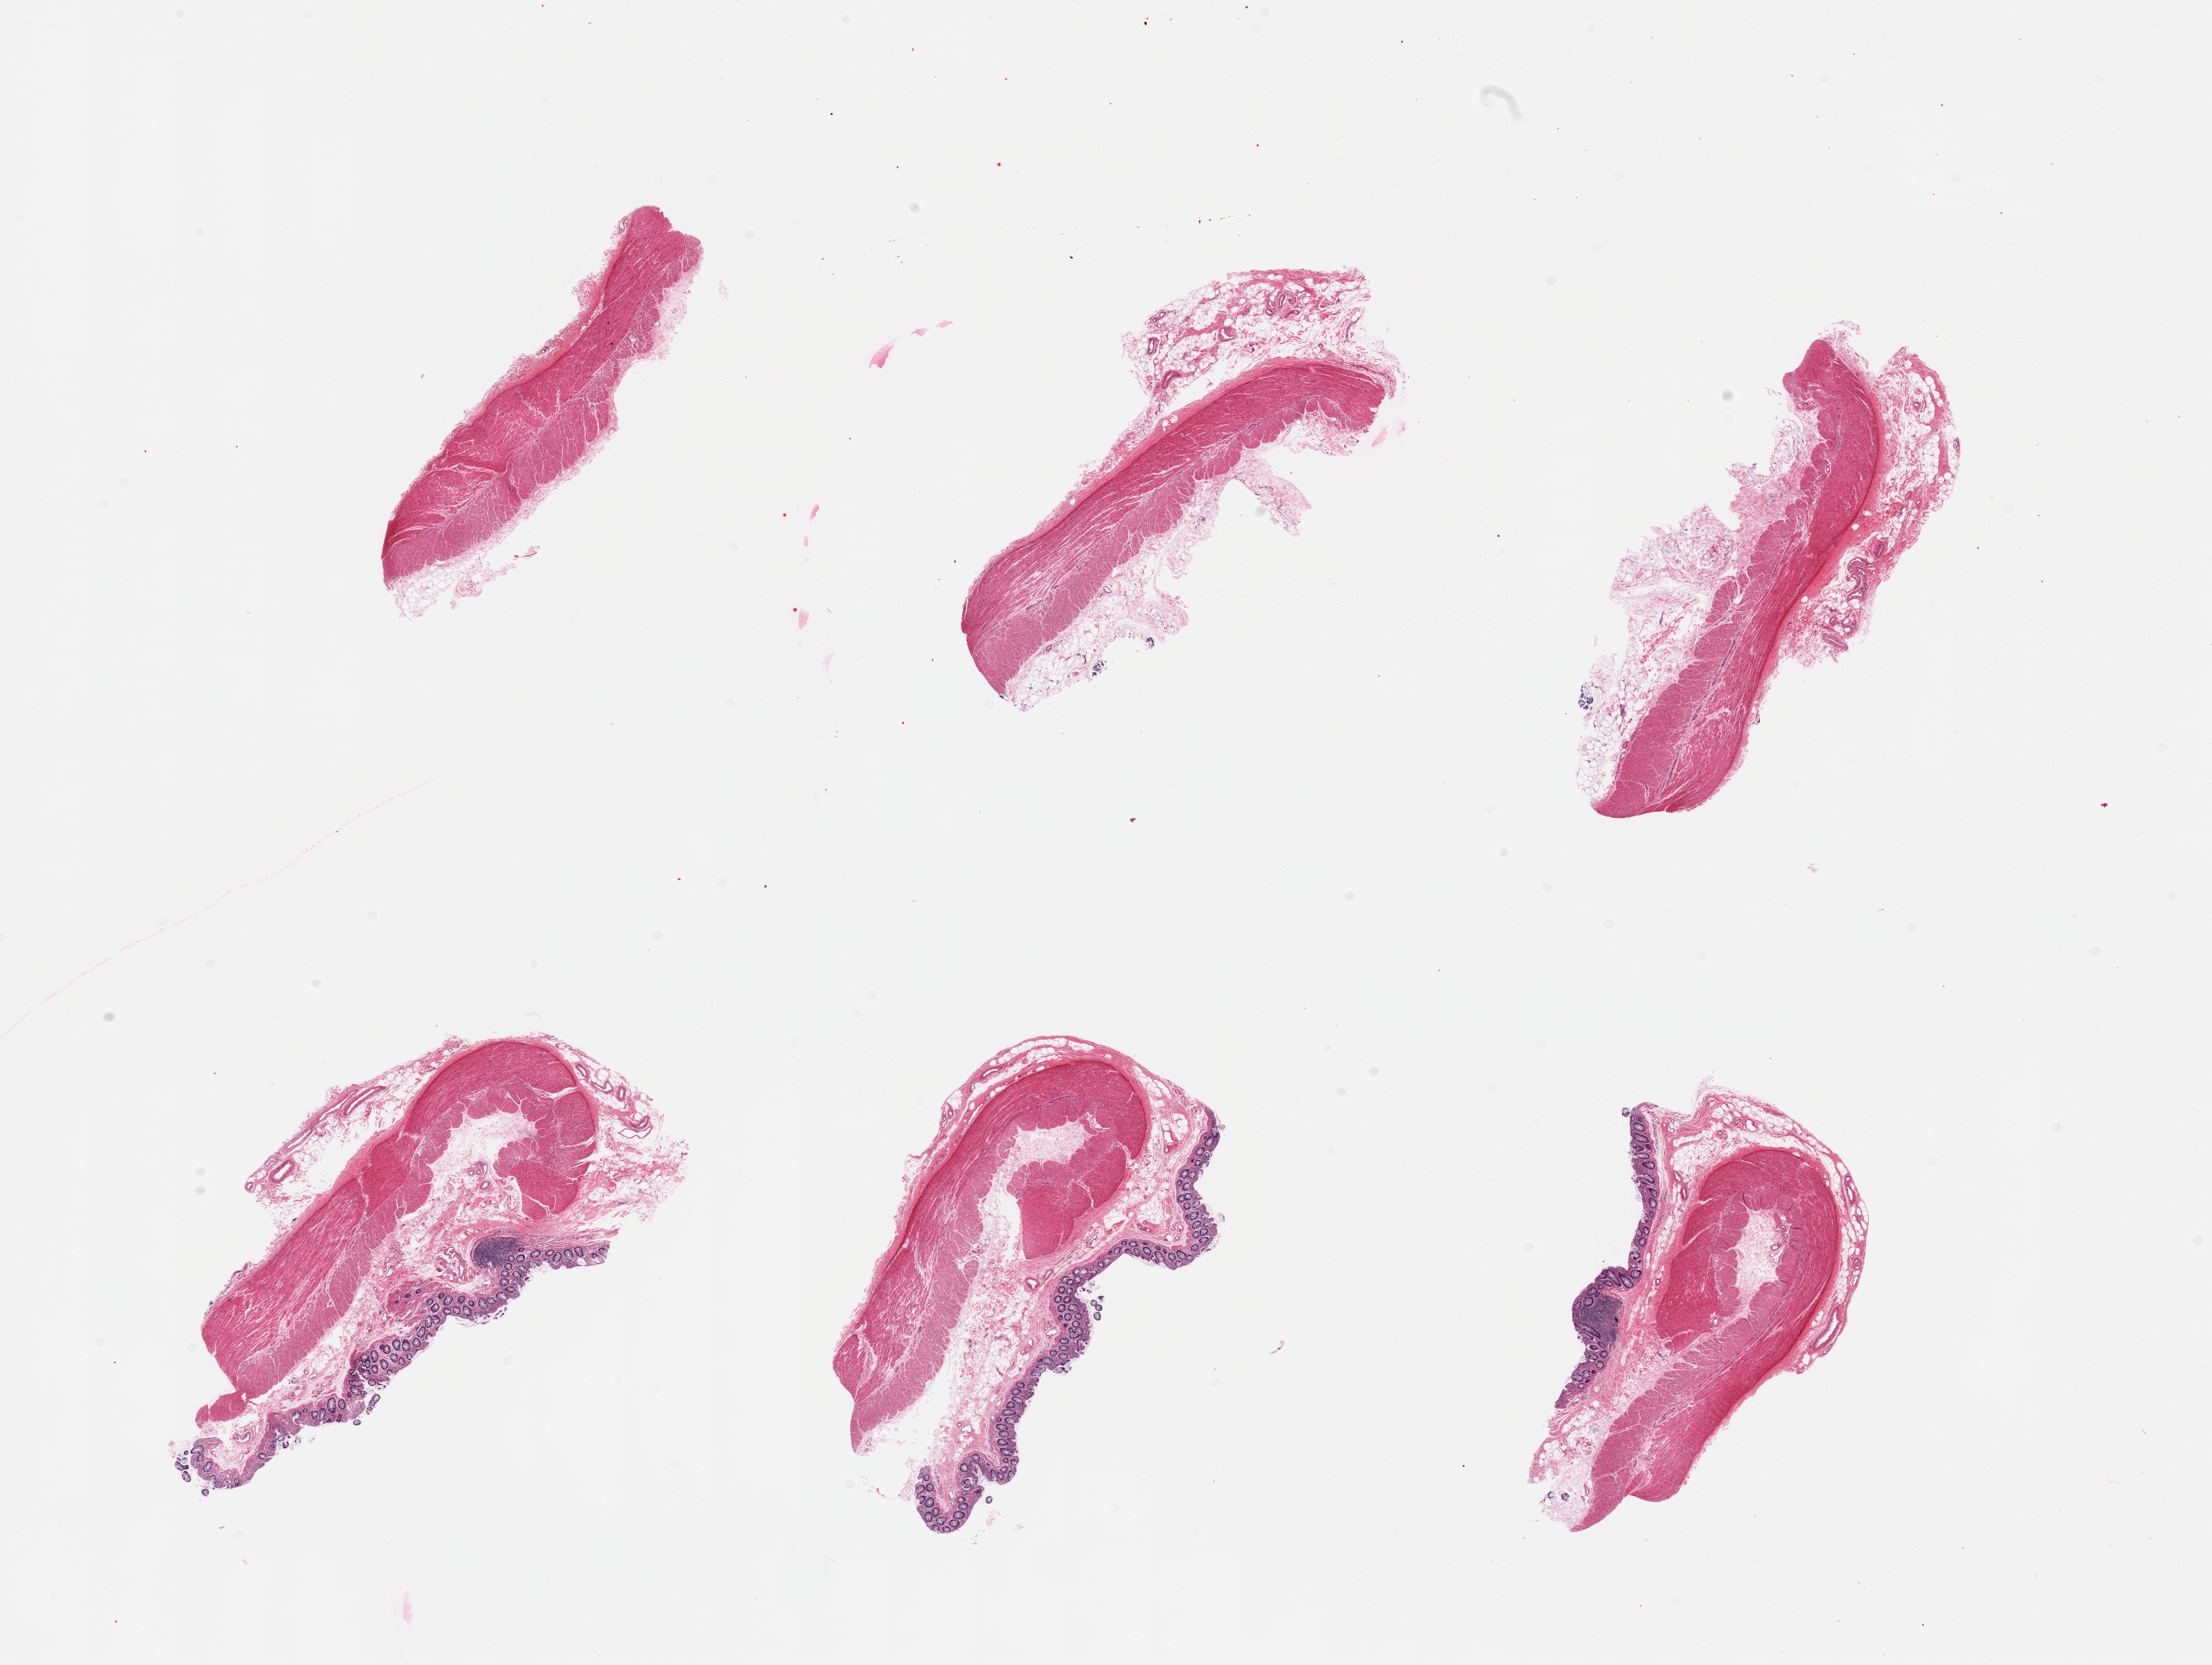
Digitized haematoxylin and eosin-stained section — shown as a low-resolution overview of the whole scanned area (about 24.6 x 18.5 mm); PAXgene-fixed, paraffin-embedded tissue; target tissue: transverse colon; tissue donor sample. Donor: female.
• review note (as recorded): 6 pieces, mucosa up to ~0.4mm, partially sloughed